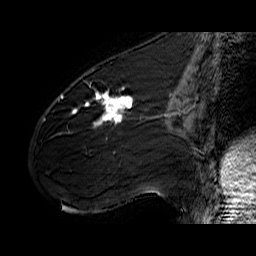
Breast MRI (dynamic contrast-enhanced), one sagittal slice. Slice 24 of 60 in the series (ordered by position). Dynamic contrast-enhanced series, time point 2 of 6 at this slice position (early post-contrast). 1.5 T. TE 6.4 ms, TR 32.9 ms. 4 mm slice thickness. 256 × 256 image matrix, field of view 200 × 200 mm. Female patient. From the clinical record (not read from this slice): setting: breast cancer imaged before/during neoadjuvant chemotherapy; receptor status: HER2-positive.
Annotated regions visible in this slice (semi-automatically segmented with operator editing):
- analysis volume of interest (the breast-tissue region the enhancement analysis was run in; not a lesion): bounding box [x1, y1, x2, y2] px = [61, 77, 141, 142]
- tumour enhancement mask (voxels above the 100 % enhancement threshold inside the analysis volume of interest): [61, 87, 134, 125]